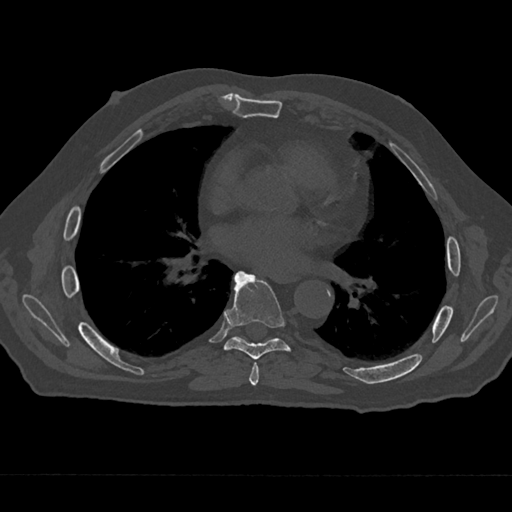
CT including the spine, one axial slice; position 367 of 797 along the scan axis; reconstruction kernel Br40s/3; bone window (W 1800 / L 400 HU); 512 × 512 image matrix, field of view 377 × 377 mm. Patient: male, 75 years. From the clinical record (not read from this slice): primary cancer: renal.
Outlined on this slice (semi-automatically segmented with operator editing):
- T6 vertebra: bounding box [x1, y1, x2, y2] px = [249, 362, 259, 386]
- T7 vertebra: [226, 271, 290, 360]